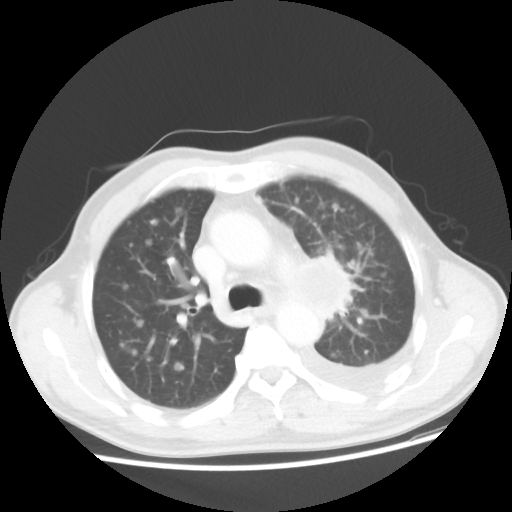
Chest CT, one axial slice. Reconstruction kernel STANDARD. 100 kVp. Lung window (W 1500 / L -600 HU). 5 mm slice thickness. 512 × 512 image matrix, field of view 362 × 362 mm. Male patient, age 55 years. Case-level facts recorded for this patient, not image findings: clinical TNM (as recorded): T2 N3 M1a; histopathological grade: G3.
Annotated regions visible in this slice (rectangle marked by the reading radiologist):
- lung tumour (recorded histology: squamous cell carcinoma): bounding box [x1, y1, x2, y2] px = [292, 250, 352, 324]